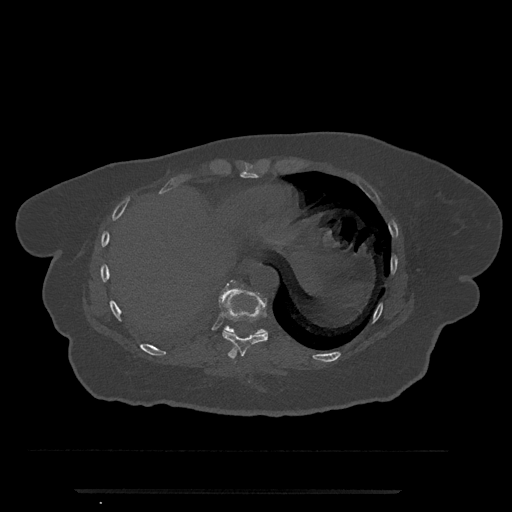
CT including the spine, one axial slice. Position 326 of 797 along the scan axis. 120 kVp. Bone window (W 1800 / L 400 HU). 512 × 512 image matrix, field of view 440 × 440 mm. Female patient, age 51 years. Case-level facts recorded for this patient, not image findings: primary cancer: neuro; vertebrae with lytic lesions (as recorded): T8.
Outlined on this slice (semi-automatic segmentation, software-assisted and operator-edited):
- T10 vertebra: bounding box [x1, y1, x2, y2] px = [223, 281, 265, 335]
- T9 vertebra: [219, 281, 268, 359]